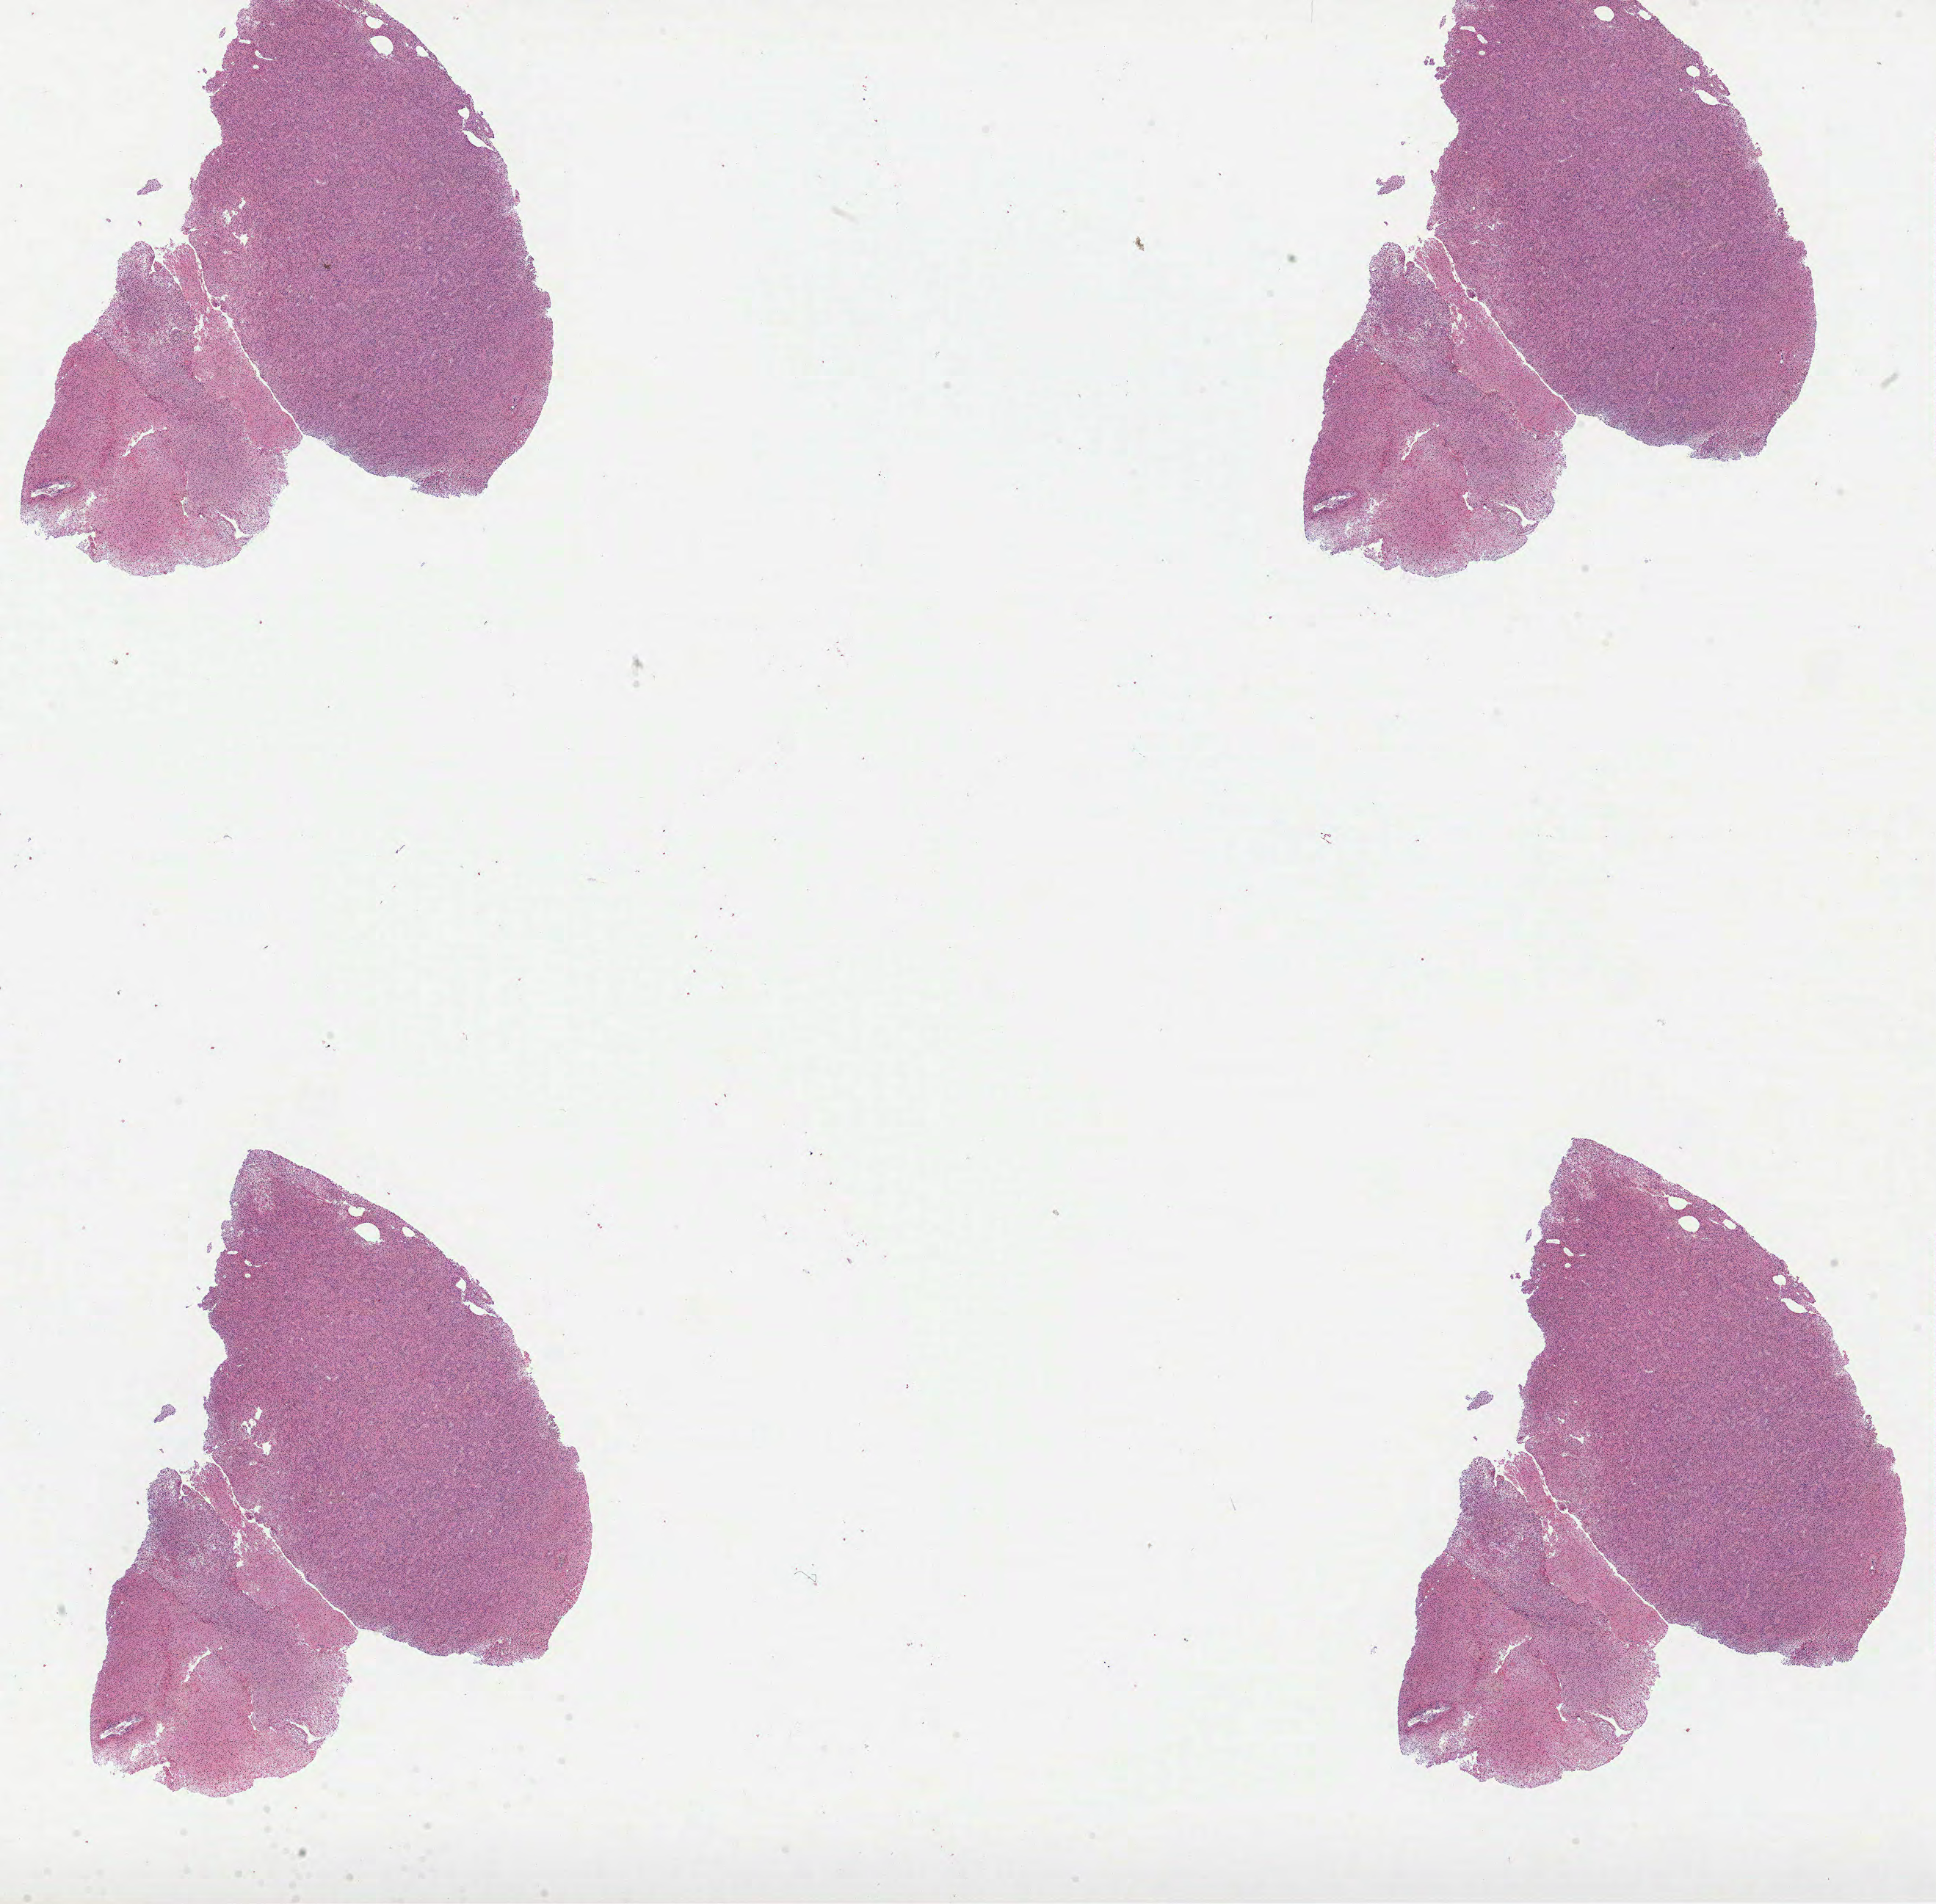
Whole-slide histology image, Hematoxylin and eosin (H&E) stained — low-resolution overview of the scanned area, about 21.3 x 20.9 mm (slide scanned at 40x). Formalin-fixed paraffin-embedded (FFPE) diagnostic section. Primary tumour sample from the brain. Female patient; age at initial diagnosis 51 years. Histologic grade: G3 (poorly differentiated).
- laterality: right
- histologic diagnosis: Astrocytoma, anaplastic (cerebrum)